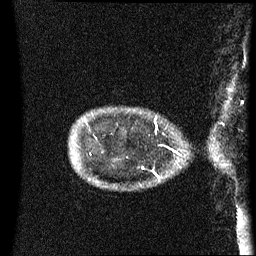
Breast MRI (dynamic contrast-enhanced), one sagittal slice. Position 9 of 60 along the scan axis. Dynamic contrast-enhanced series, image 2 of 3 at this slice position (ordered by acquisition). 1.5 T. TE 4.2 ms, TR 8.4 ms. 2.5 mm slice thickness. 256 × 256 image matrix, field of view 220 × 220 mm. Patient: female, 41 years. From the clinical record (not read from this slice): setting: breast cancer imaged before/during neoadjuvant chemotherapy; receptor status: HER2-positive.
Annotated regions visible in this slice (semi-automatically segmented with operator editing):
- analysis volume of interest (the breast-tissue region the enhancement analysis was run in; not a lesion): box from (x=122, y=108) to (x=182, y=137) px
- tumour enhancement mask (voxels above the 70 % enhancement threshold inside the analysis volume of interest): (x=155, y=118)–(x=158, y=129)